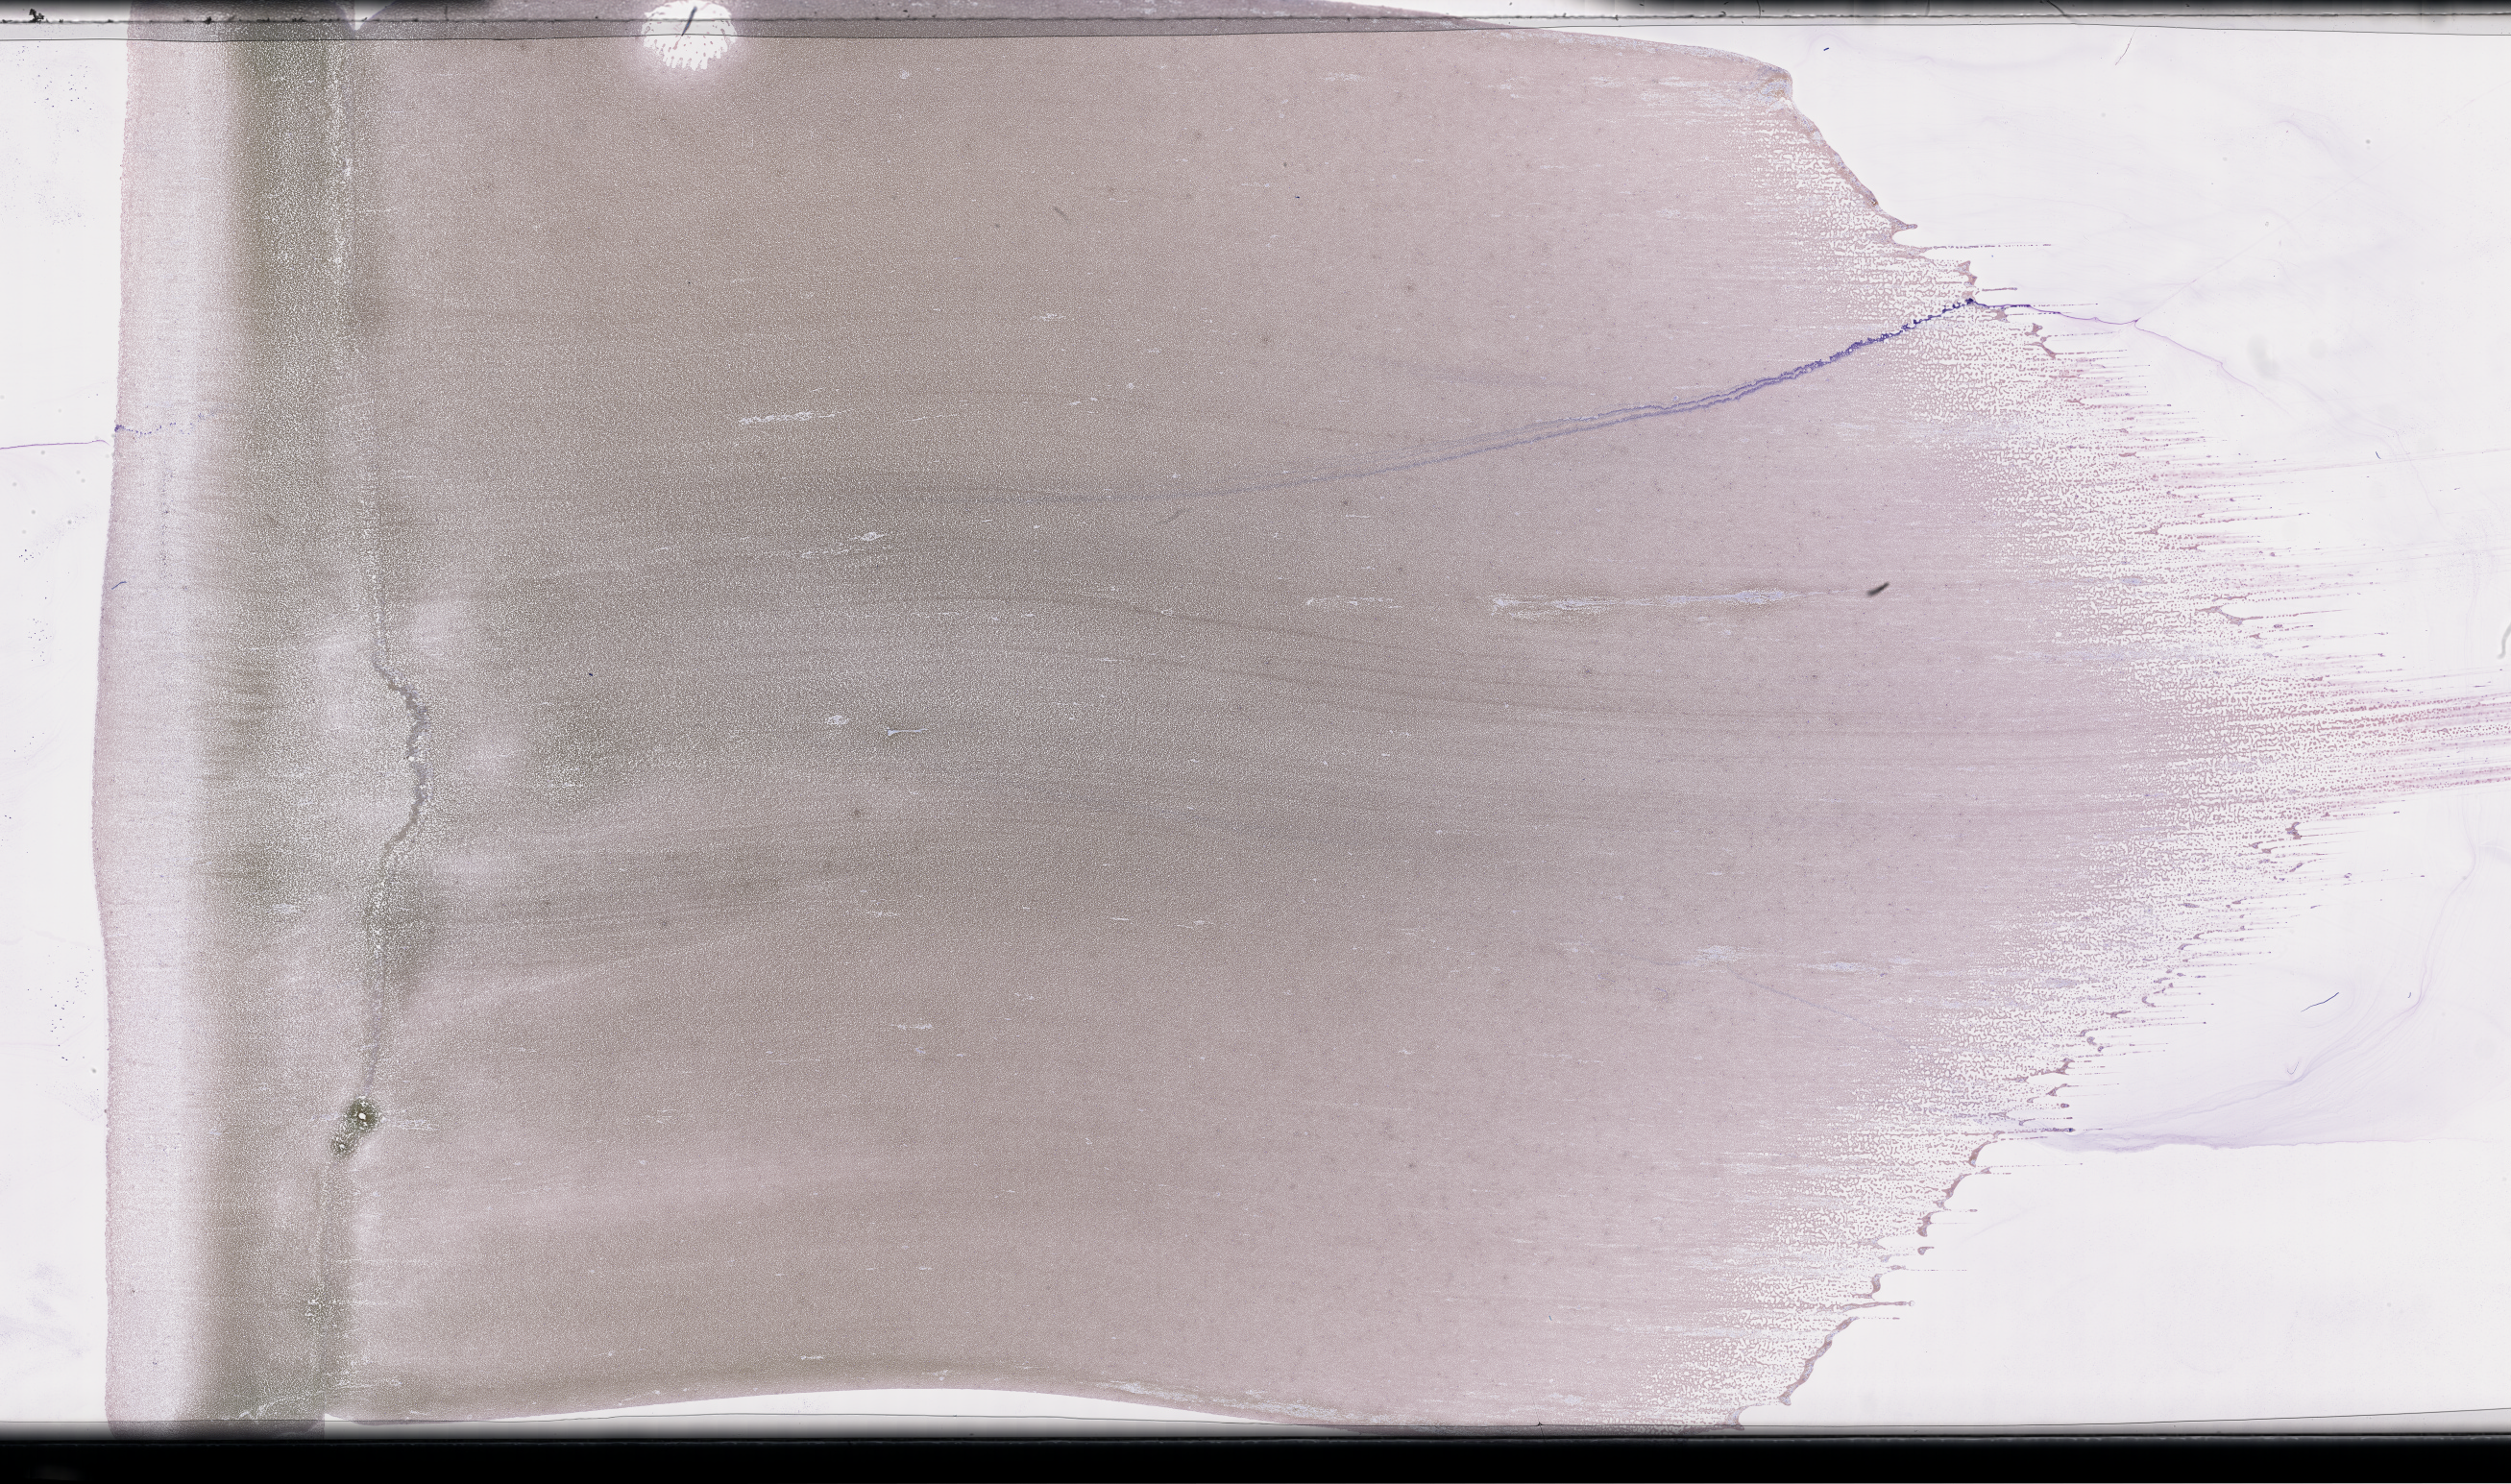
Wright-Giemsa-stained whole blood smear, whole-slide image — shown as a low-resolution overview of the whole scanned area (about 42.2 x 25.0 mm). Patient: female.
Patient diagnosis: Plasma Cell Myeloma.